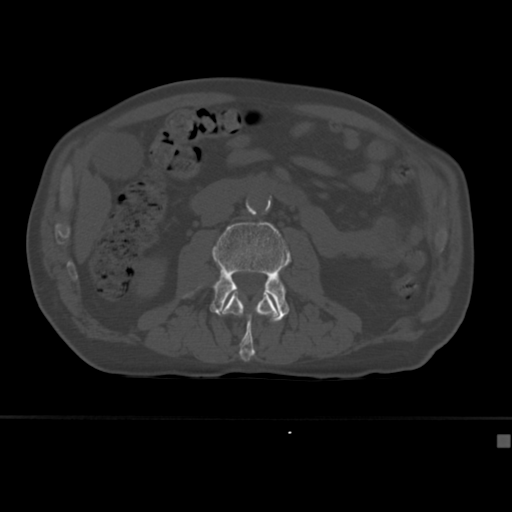
CT including the spine, one axial slice; slice 136 of 430 in the series (ordered by position); reconstruction kernel Br40s; 120 kVp; bone window (W 1800 / L 400 HU); 1.5 mm slice thickness; 512 × 512 image matrix, field of view 337 × 337 mm. Male patient, age 64 years. Case-level facts recorded for this patient, not image findings: primary cancer: uterus; vertebrae with lytic lesions (as recorded): T1, T4, T5, T7, L5.
Annotated regions visible in this slice (semi-automatic segmentation, software-assisted and operator-edited):
- L2 vertebra: box from (x=219, y=292) to (x=278, y=362) px
- L3 vertebra: (x=183, y=221)–(x=292, y=323)